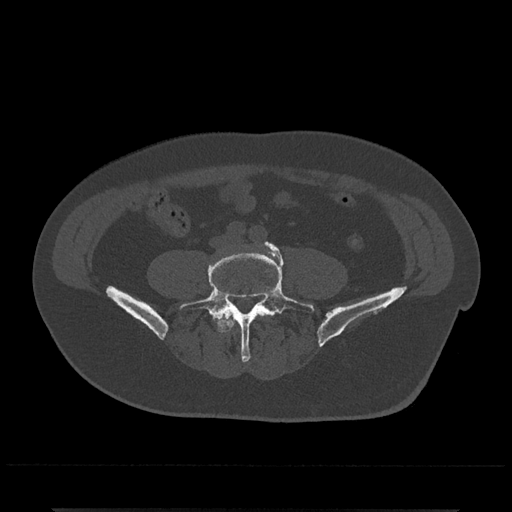
CT including the spine, one axial slice; position 99 of 797 along the scan axis; 120 kVp; bone window (W 1800 / L 400 HU); 0.5 mm slice thickness; 512 × 512 image matrix. Male patient, age 67 years. Case-level facts recorded for this patient, not image findings: primary cancer: prostate.
Annotated regions visible in this slice (semi-automatically segmented with operator editing):
- L4 vertebra: box from (x=219, y=312) to (x=264, y=332) px
- L5 vertebra: (x=179, y=242)–(x=315, y=362)